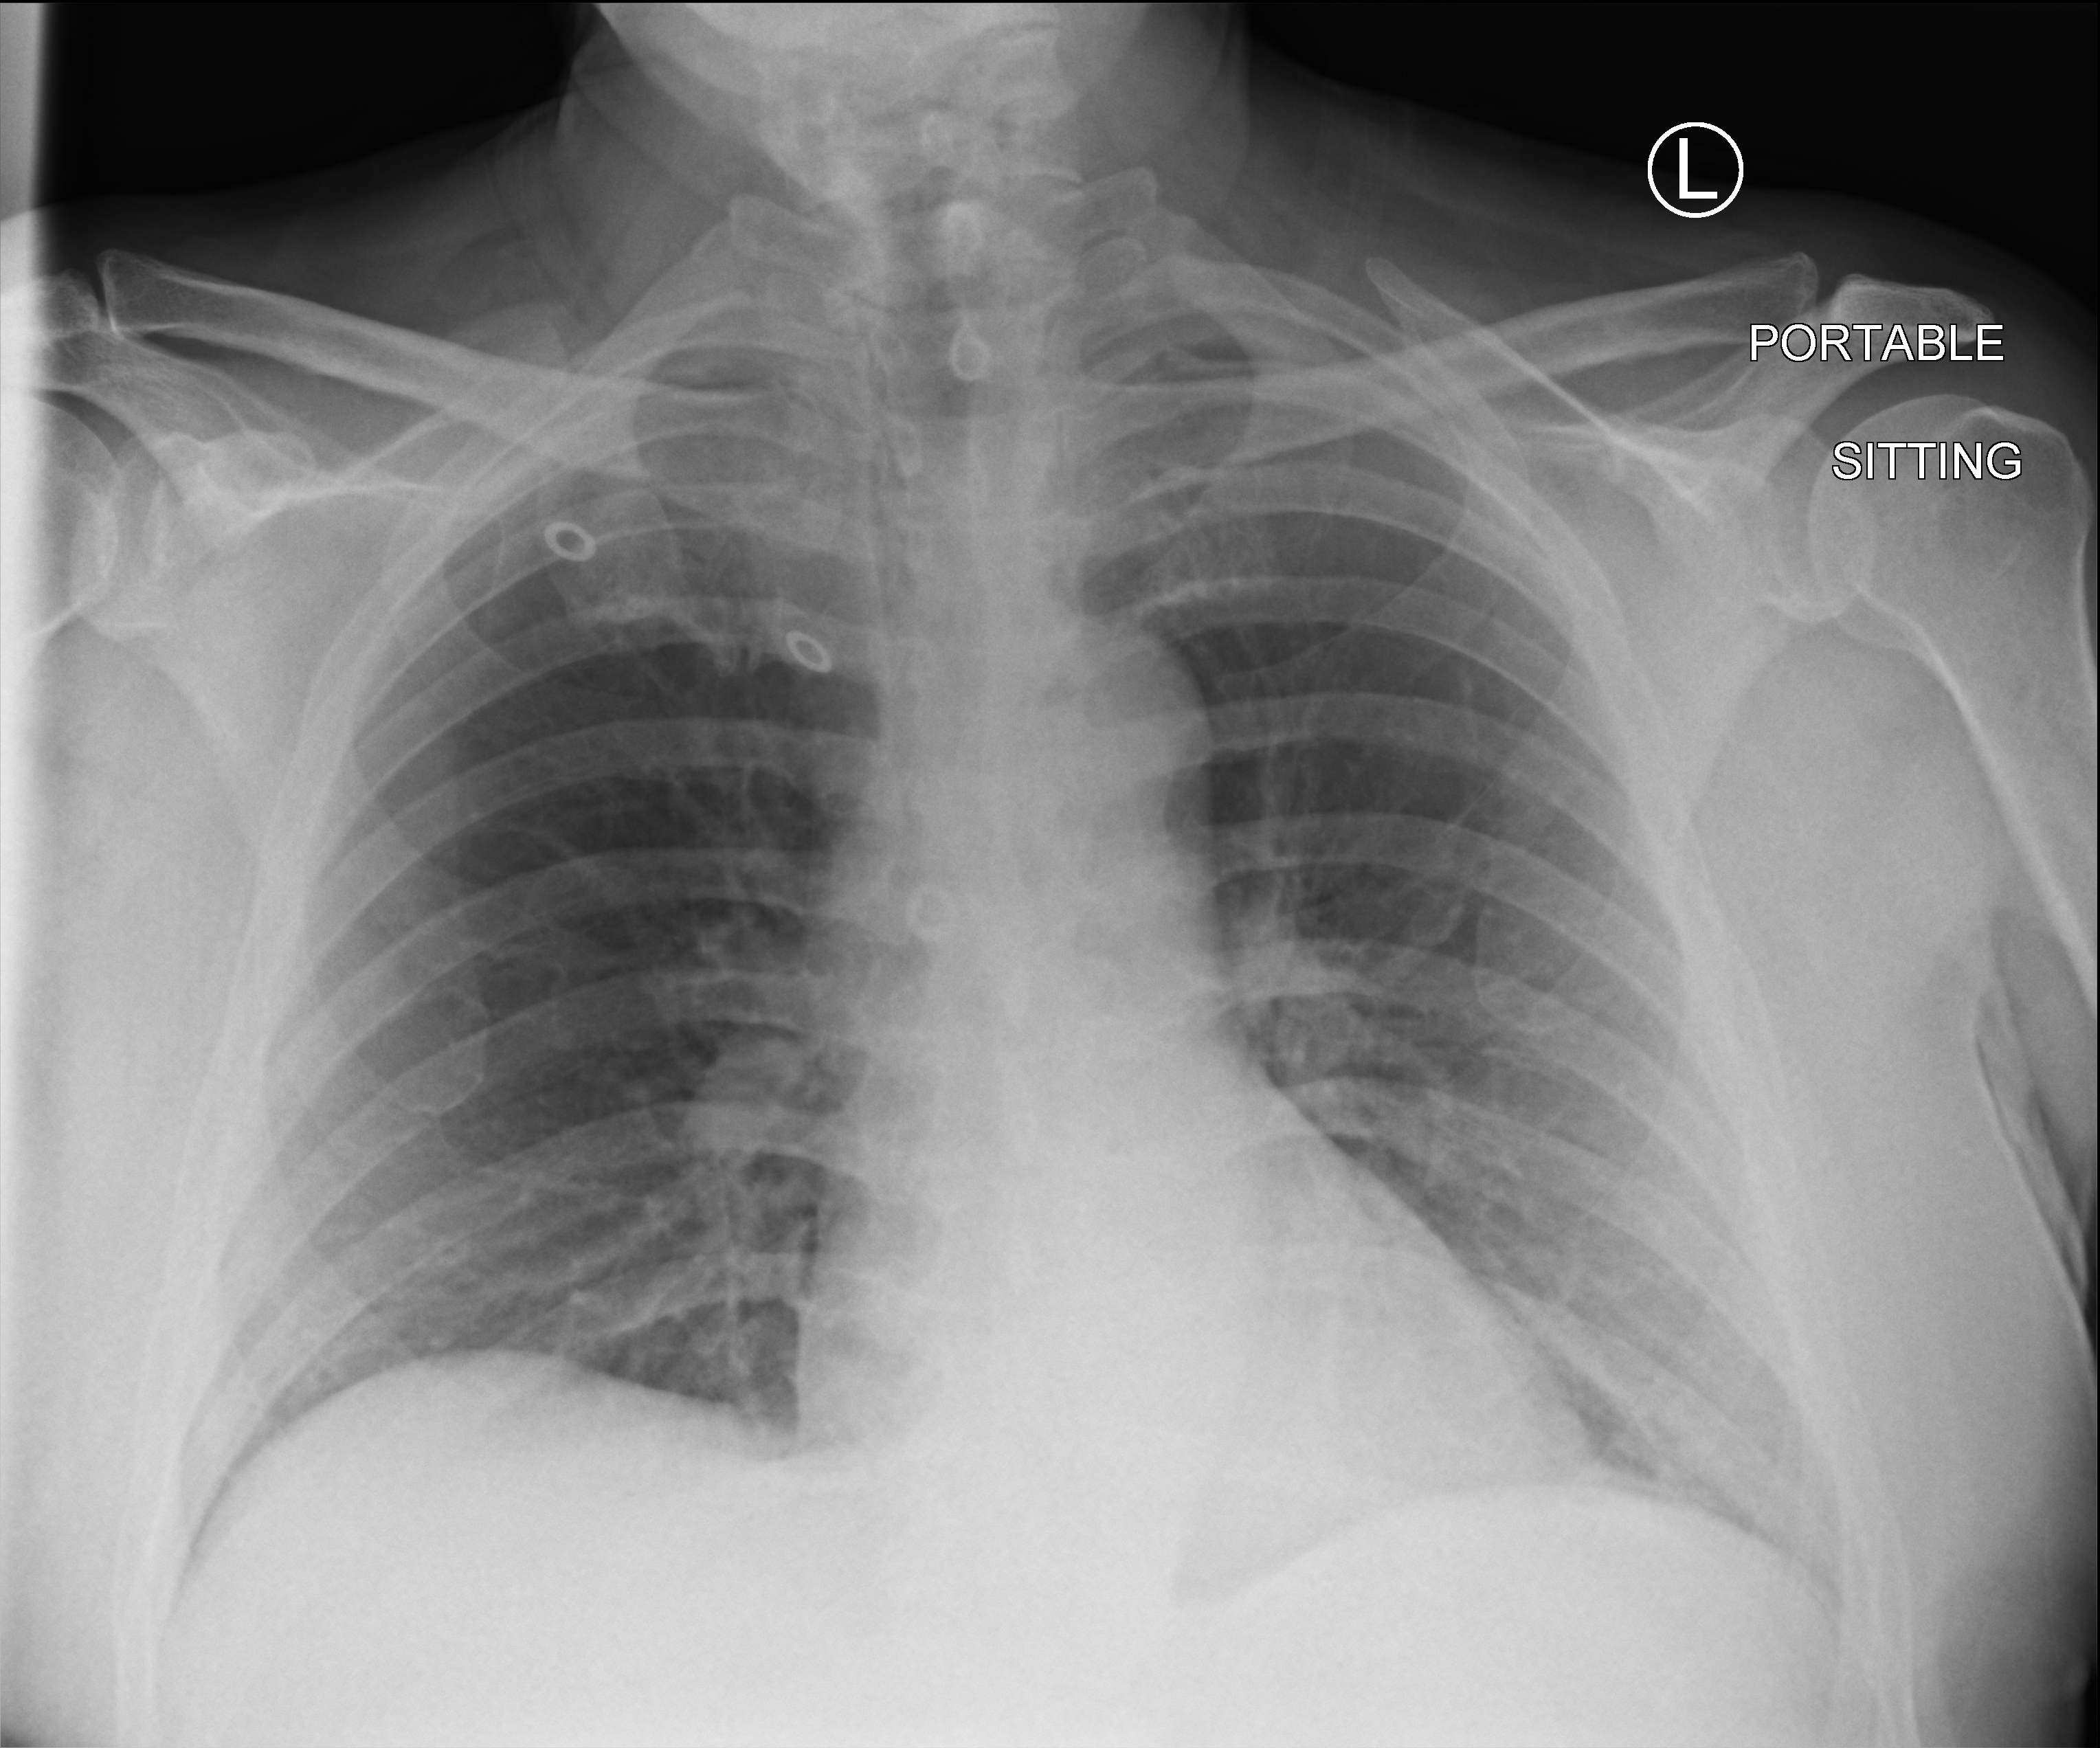
Portable chest radiograph, anteroposterior (AP) projection. Male patient hospitalised with COVID-19, age 60–74 years.
Admission-level facts for this patient (not findings on this image; timing relative to this image not recorded):
- mechanically ventilated during this hospital stay: no
- admitted to intensive care during this hospital stay: no